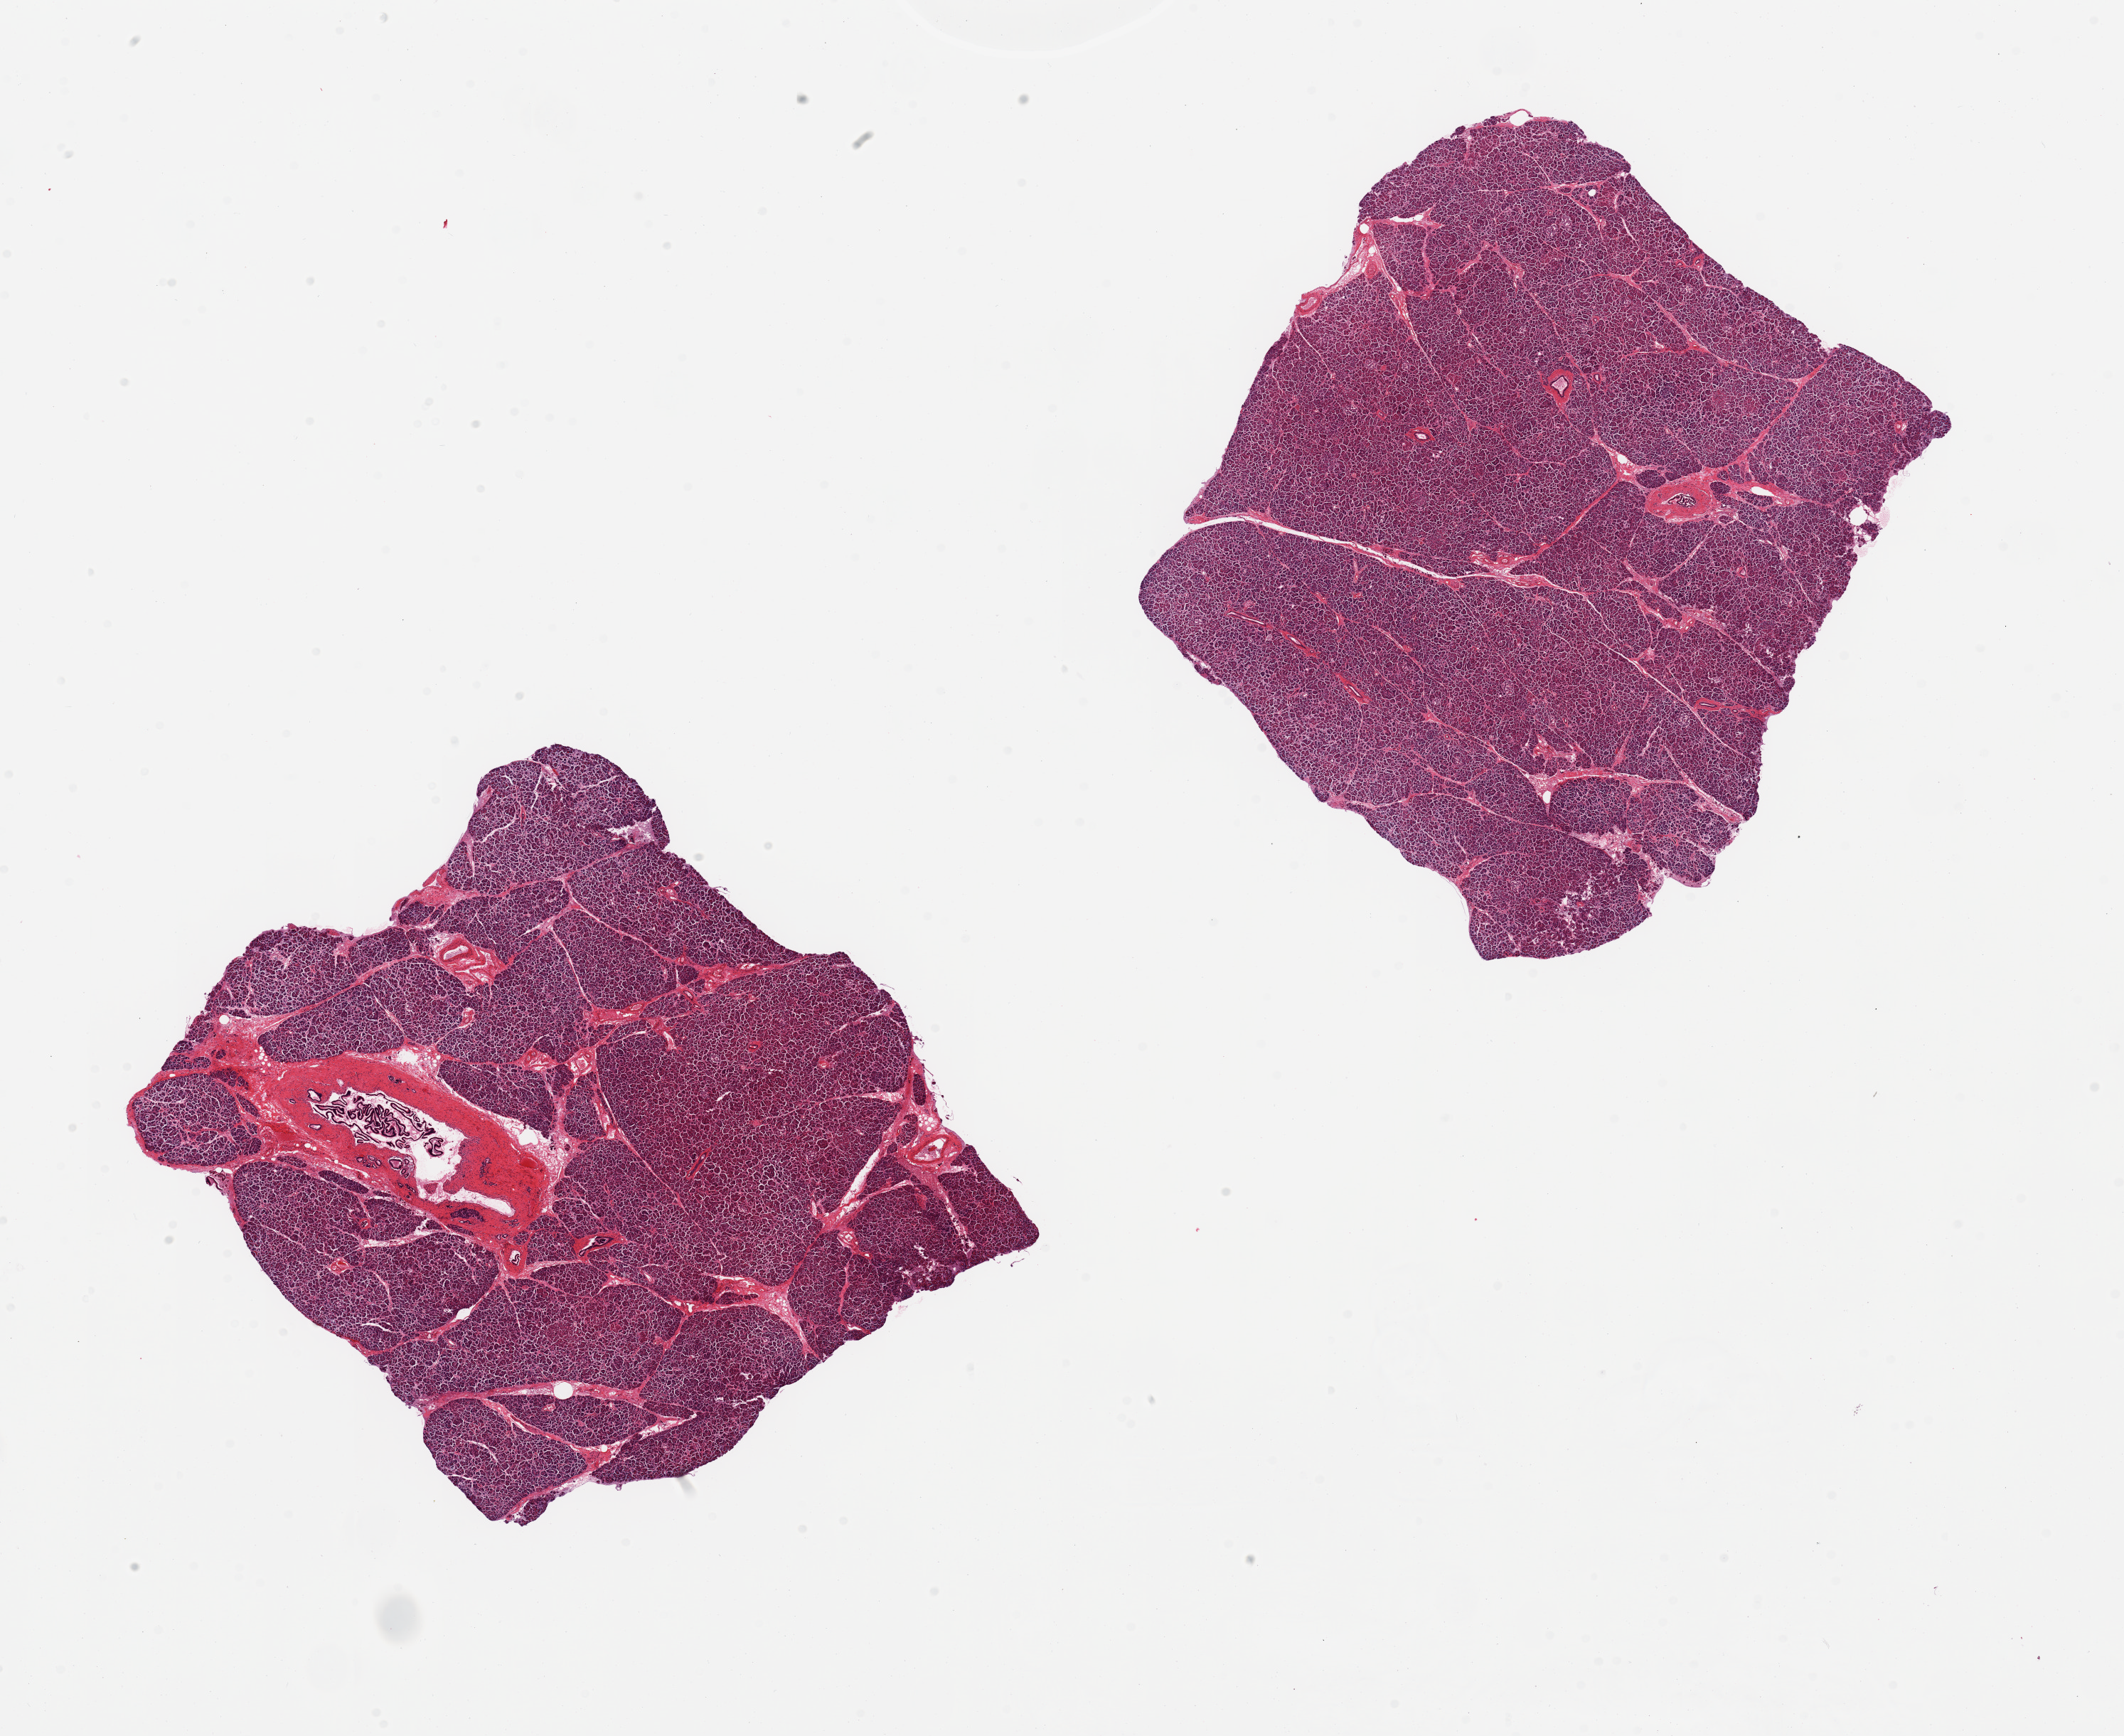
Whole-slide image, H&E stain, brightfield, shown as a low-resolution overview of the whole scanned area (about 23.6 x 19.3 mm). PAXgene-fixed paraffin-embedded (PFPE) section. Section of pancreas (target tissue). Tissue donor sample. Donor sex: male.
Reviewer comment on this tissue sample: 2 pieces moderate autolysis; An occasional Islet is visible, not well preserved.